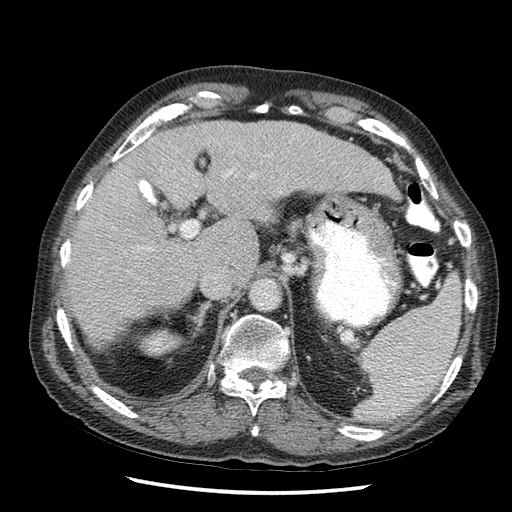
Contrast-enhanced abdominal CT (liver protocol), one axial slice. Slice 32 of 67 in the series (ordered by position). Reconstruction kernel STANDARD. Soft-tissue window (W 400 / L 40 HU). 2.5 mm slice thickness. 512 × 512 image matrix. From the clinical record (not read from this slice): diagnosis: hepatocellular carcinoma (patient treated with transarterial chemoembolisation; whether this scan precedes or follows treatment is not stated here); TNM stage (as recorded): Stage-I; Child-Pugh class: A; tumour differentiation: moderately differentiated; tumour nodularity: uninodular.
Annotated regions visible in this slice (semi-automatically segmented with operator editing):
- liver parenchyma outside the tumour (the mass and vessels are separate outlines, so this box may not span the whole liver): bounding box [x1, y1, x2, y2] px = [64, 118, 402, 366]
- liver vessels: [125, 144, 224, 246]